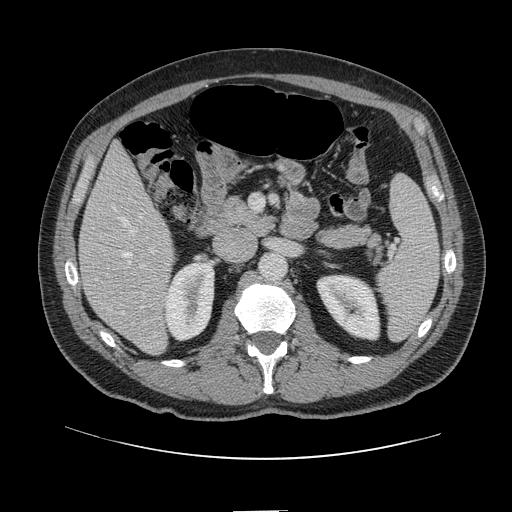
Contrast-enhanced abdominal CT, one axial slice; slice 53 of 161 in the series (ordered by position); intravenous contrast given; soft-tissue window (W 400 / L 40 HU); 2.5 mm slice thickness; 512 × 512 image matrix, field of view 412 × 412 mm. Male patient, age 66 years. Case-level facts recorded for this patient, not image findings: diagnosis: colorectal cancer liver metastases, imaged before liver resection; multiple liver metastases: no; largest metastasis: 3.5 cm; disease in both lobes: no.
Outlined on this slice (outlined manually by an expert reader):
- hepatic veins: bounding box [x1, y1, x2, y2] px = [115, 208, 134, 257]
- liver: [80, 145, 175, 354]
- planned liver remnant (the part of the liver to remain after resection): [80, 146, 164, 278]
- portal vein (with intrahepatic branches): [127, 247, 157, 297]